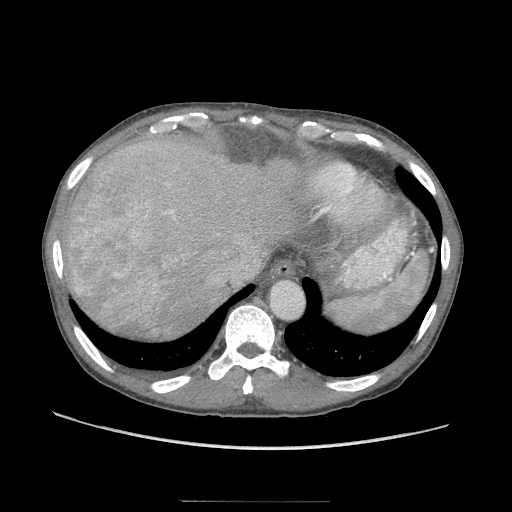
Contrast-enhanced abdominal CT (liver protocol), one axial slice. Reconstruction kernel STANDARD. Soft-tissue window (W 400 / L 40 HU). 2.5 mm slice thickness. 512 × 512 image matrix, field of view 380 × 380 mm. From the clinical record (not read from this slice): diagnosis: hepatocellular carcinoma (patient treated with transarterial chemoembolisation; whether this scan precedes or follows treatment is not stated here); TNM stage (as recorded): Stage-IIIA; Child-Pugh class: A; tumour differentiation: moderately differentiated; tumour nodularity: multinodular.
Annotated regions visible in this slice (semi-automatic segmentation, software-assisted and operator-edited):
- abdominal aorta: bounding box (x1, y1, x2, y2) in pixels: (270, 282, 303, 318)
- liver parenchyma outside the tumour (the mass and vessels are separate outlines, so this box may not span the whole liver): (62, 128, 292, 339)
- mass: (69, 175, 182, 288)
- liver vessels: (107, 283, 156, 288)